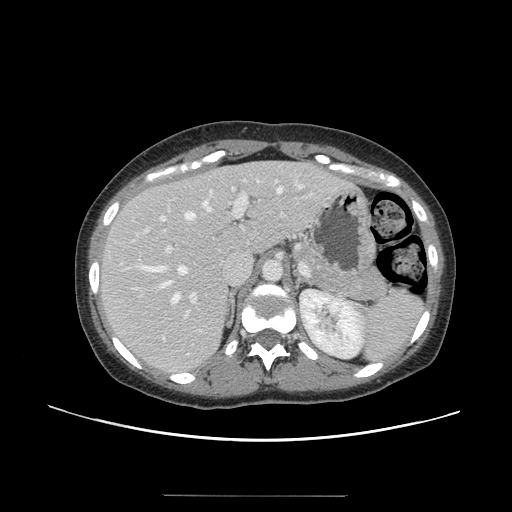
Contrast-enhanced abdominal CT, one axial slice. Position 96 of 144 along the scan axis. Intravenous contrast given. Soft-tissue window (W 400 / L 40 HU). 2.5 mm slice thickness. 512 × 512 image matrix, field of view 380 × 380 mm. Female patient, age 53 years. From the clinical record (not read from this slice): diagnosis: colorectal cancer liver metastases, imaged before liver resection.
Structures marked on this image (outlined manually by an expert reader):
- hepatic veins: box from (x=140, y=185) to (x=303, y=303) px
- liver: (x=98, y=162)–(x=344, y=374)
- planned liver remnant (the part of the liver to remain after resection): (x=98, y=162)–(x=308, y=300)
- portal vein (with intrahepatic branches): (x=137, y=180)–(x=278, y=318)